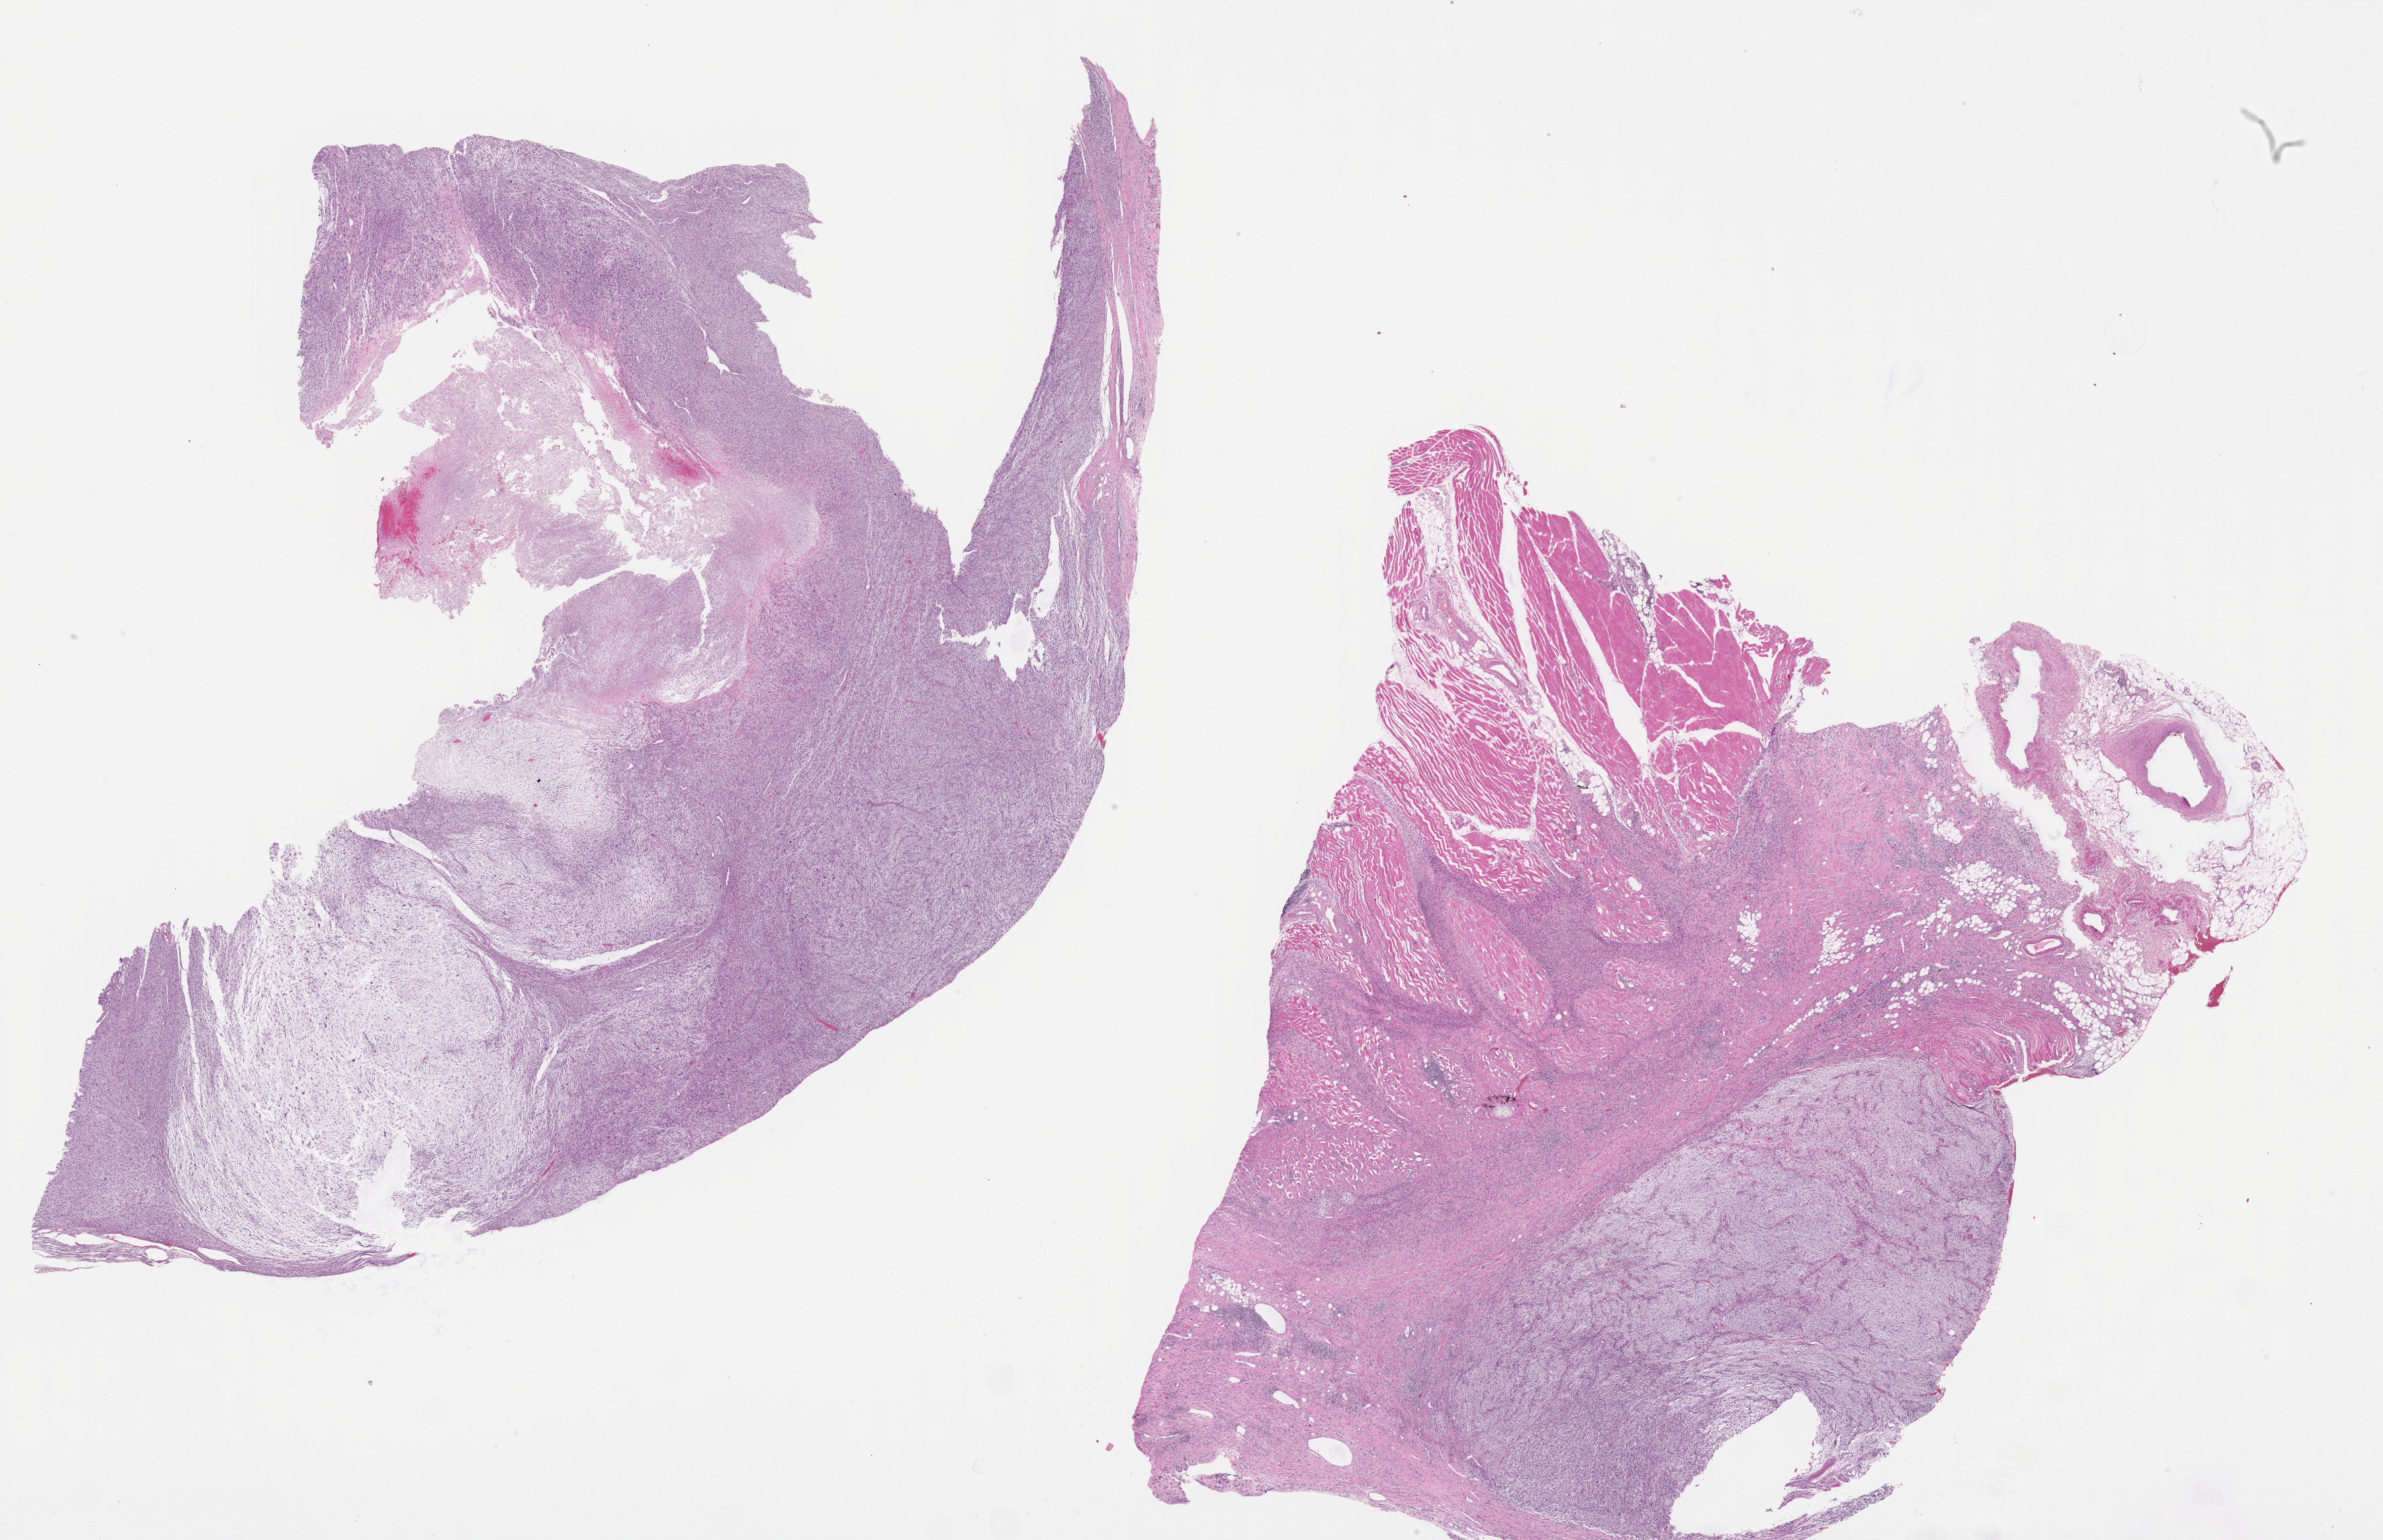
Digitized H&E-stained tissue section (whole slide) — shown as a low-resolution overview of the whole scanned area (about 28.7 x 18.5 mm, acquisition: 40x scan). Formalin-fixed paraffin-embedded (FFPE) diagnostic section. Primary tumour sample from the connective, subcutaneous and other soft tissues. Male patient; age at initial diagnosis 61 years.
Pathologic diagnosis: Fibromyxosarcoma.